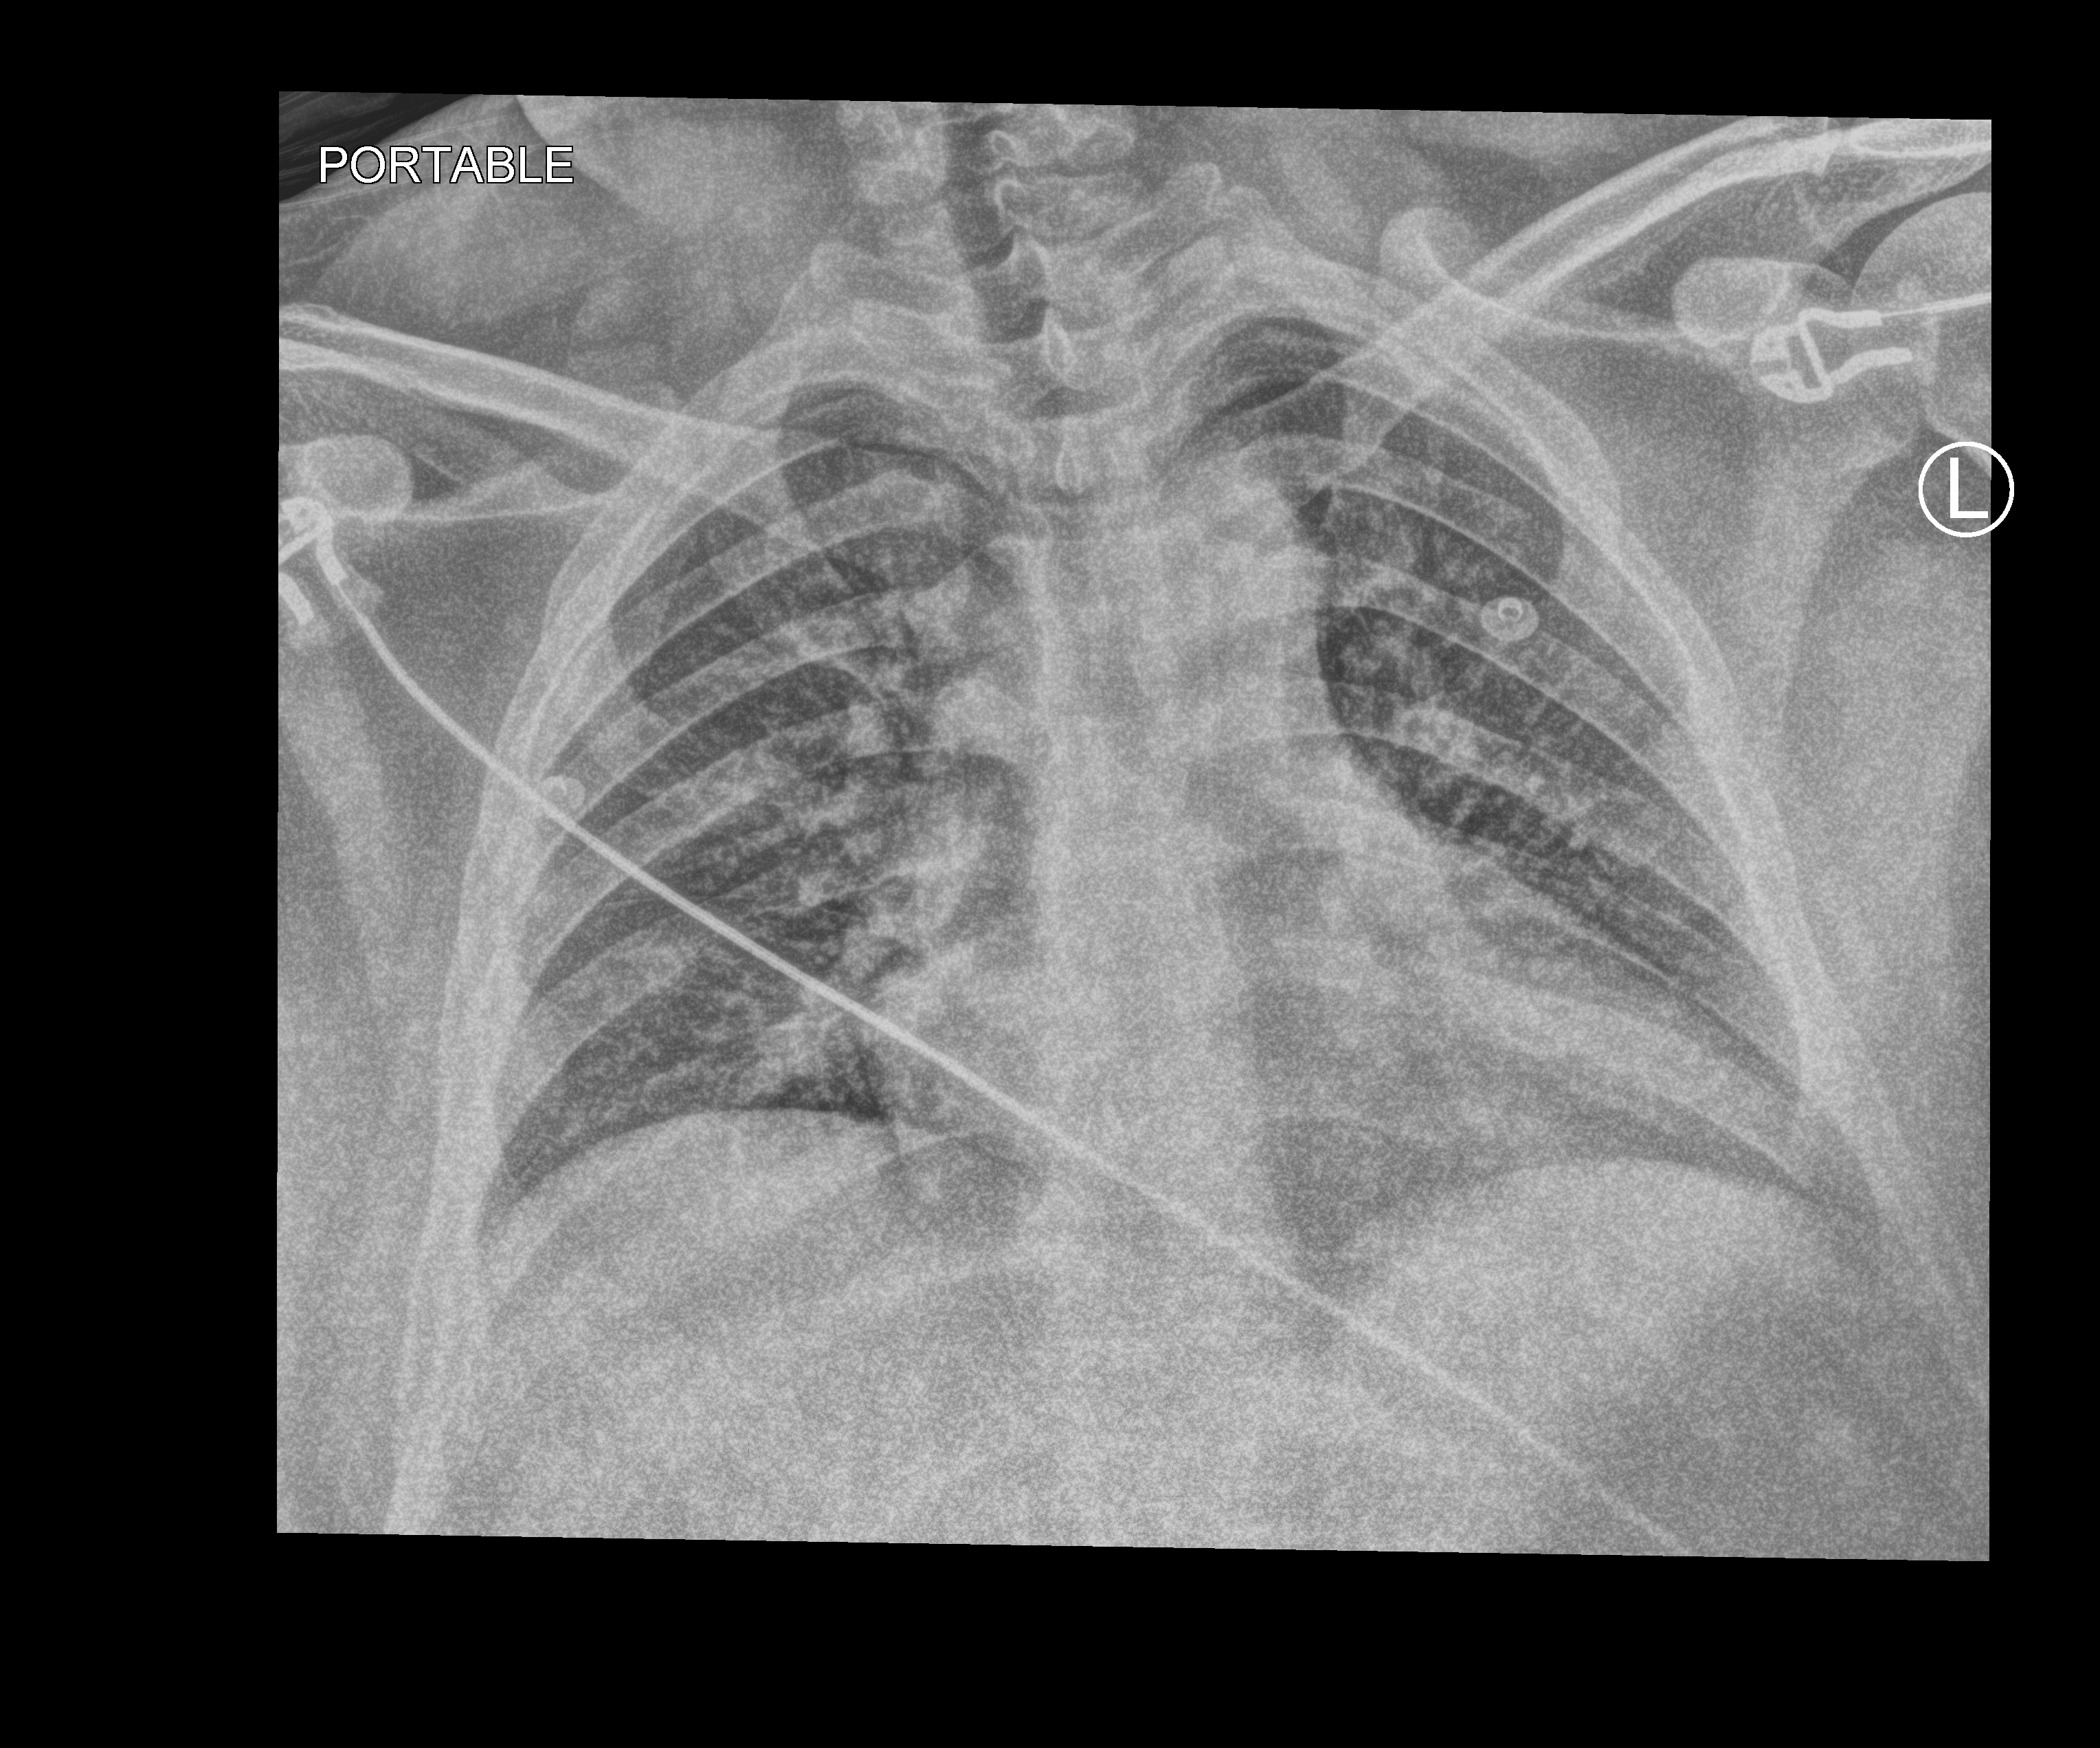
Bedside chest radiograph (computed radiography). Patient hospitalised with COVID-19; male, aged 18–59 years.
From the hospital-stay record, not from the radiograph (when in the stay this image was taken is not recorded): admitted to intensive care during this hospital stay: no.